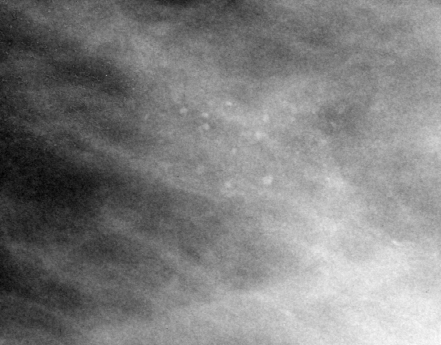
Region of interest cut from a scanned film mammogram (one marked finding), left breast, MLO view, BI-RADS breast density category 3 (scale 1–4).
Finding: calcifications, morphology punctate, distribution segmental; BI-RADS assessment category 4; subtlety rating 3 on a 1 (subtle) to 5 (obvious) scale; pathology (as recorded): benign.